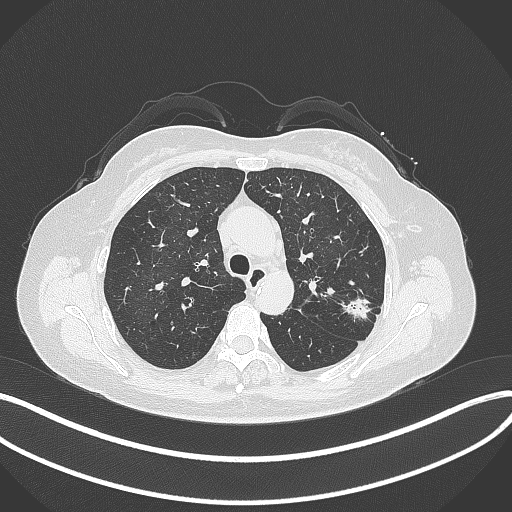
Chest CT, one axial slice; position 231 of 319 along the scan axis; 120 kVp; lung window (W 1500 / L -600 HU); 1 mm slice thickness; 512 × 512 image matrix, field of view 400 × 400 mm. Patient: female, 60 years. From the clinical record (not read from this slice): clinical TNM (as recorded): T1c N0 M0.
Structures marked on this image (rectangle marked by the reading radiologist):
- lung tumour (recorded histology: adenocarcinoma): bounding box [x1, y1, x2, y2] px = [339, 291, 373, 322]